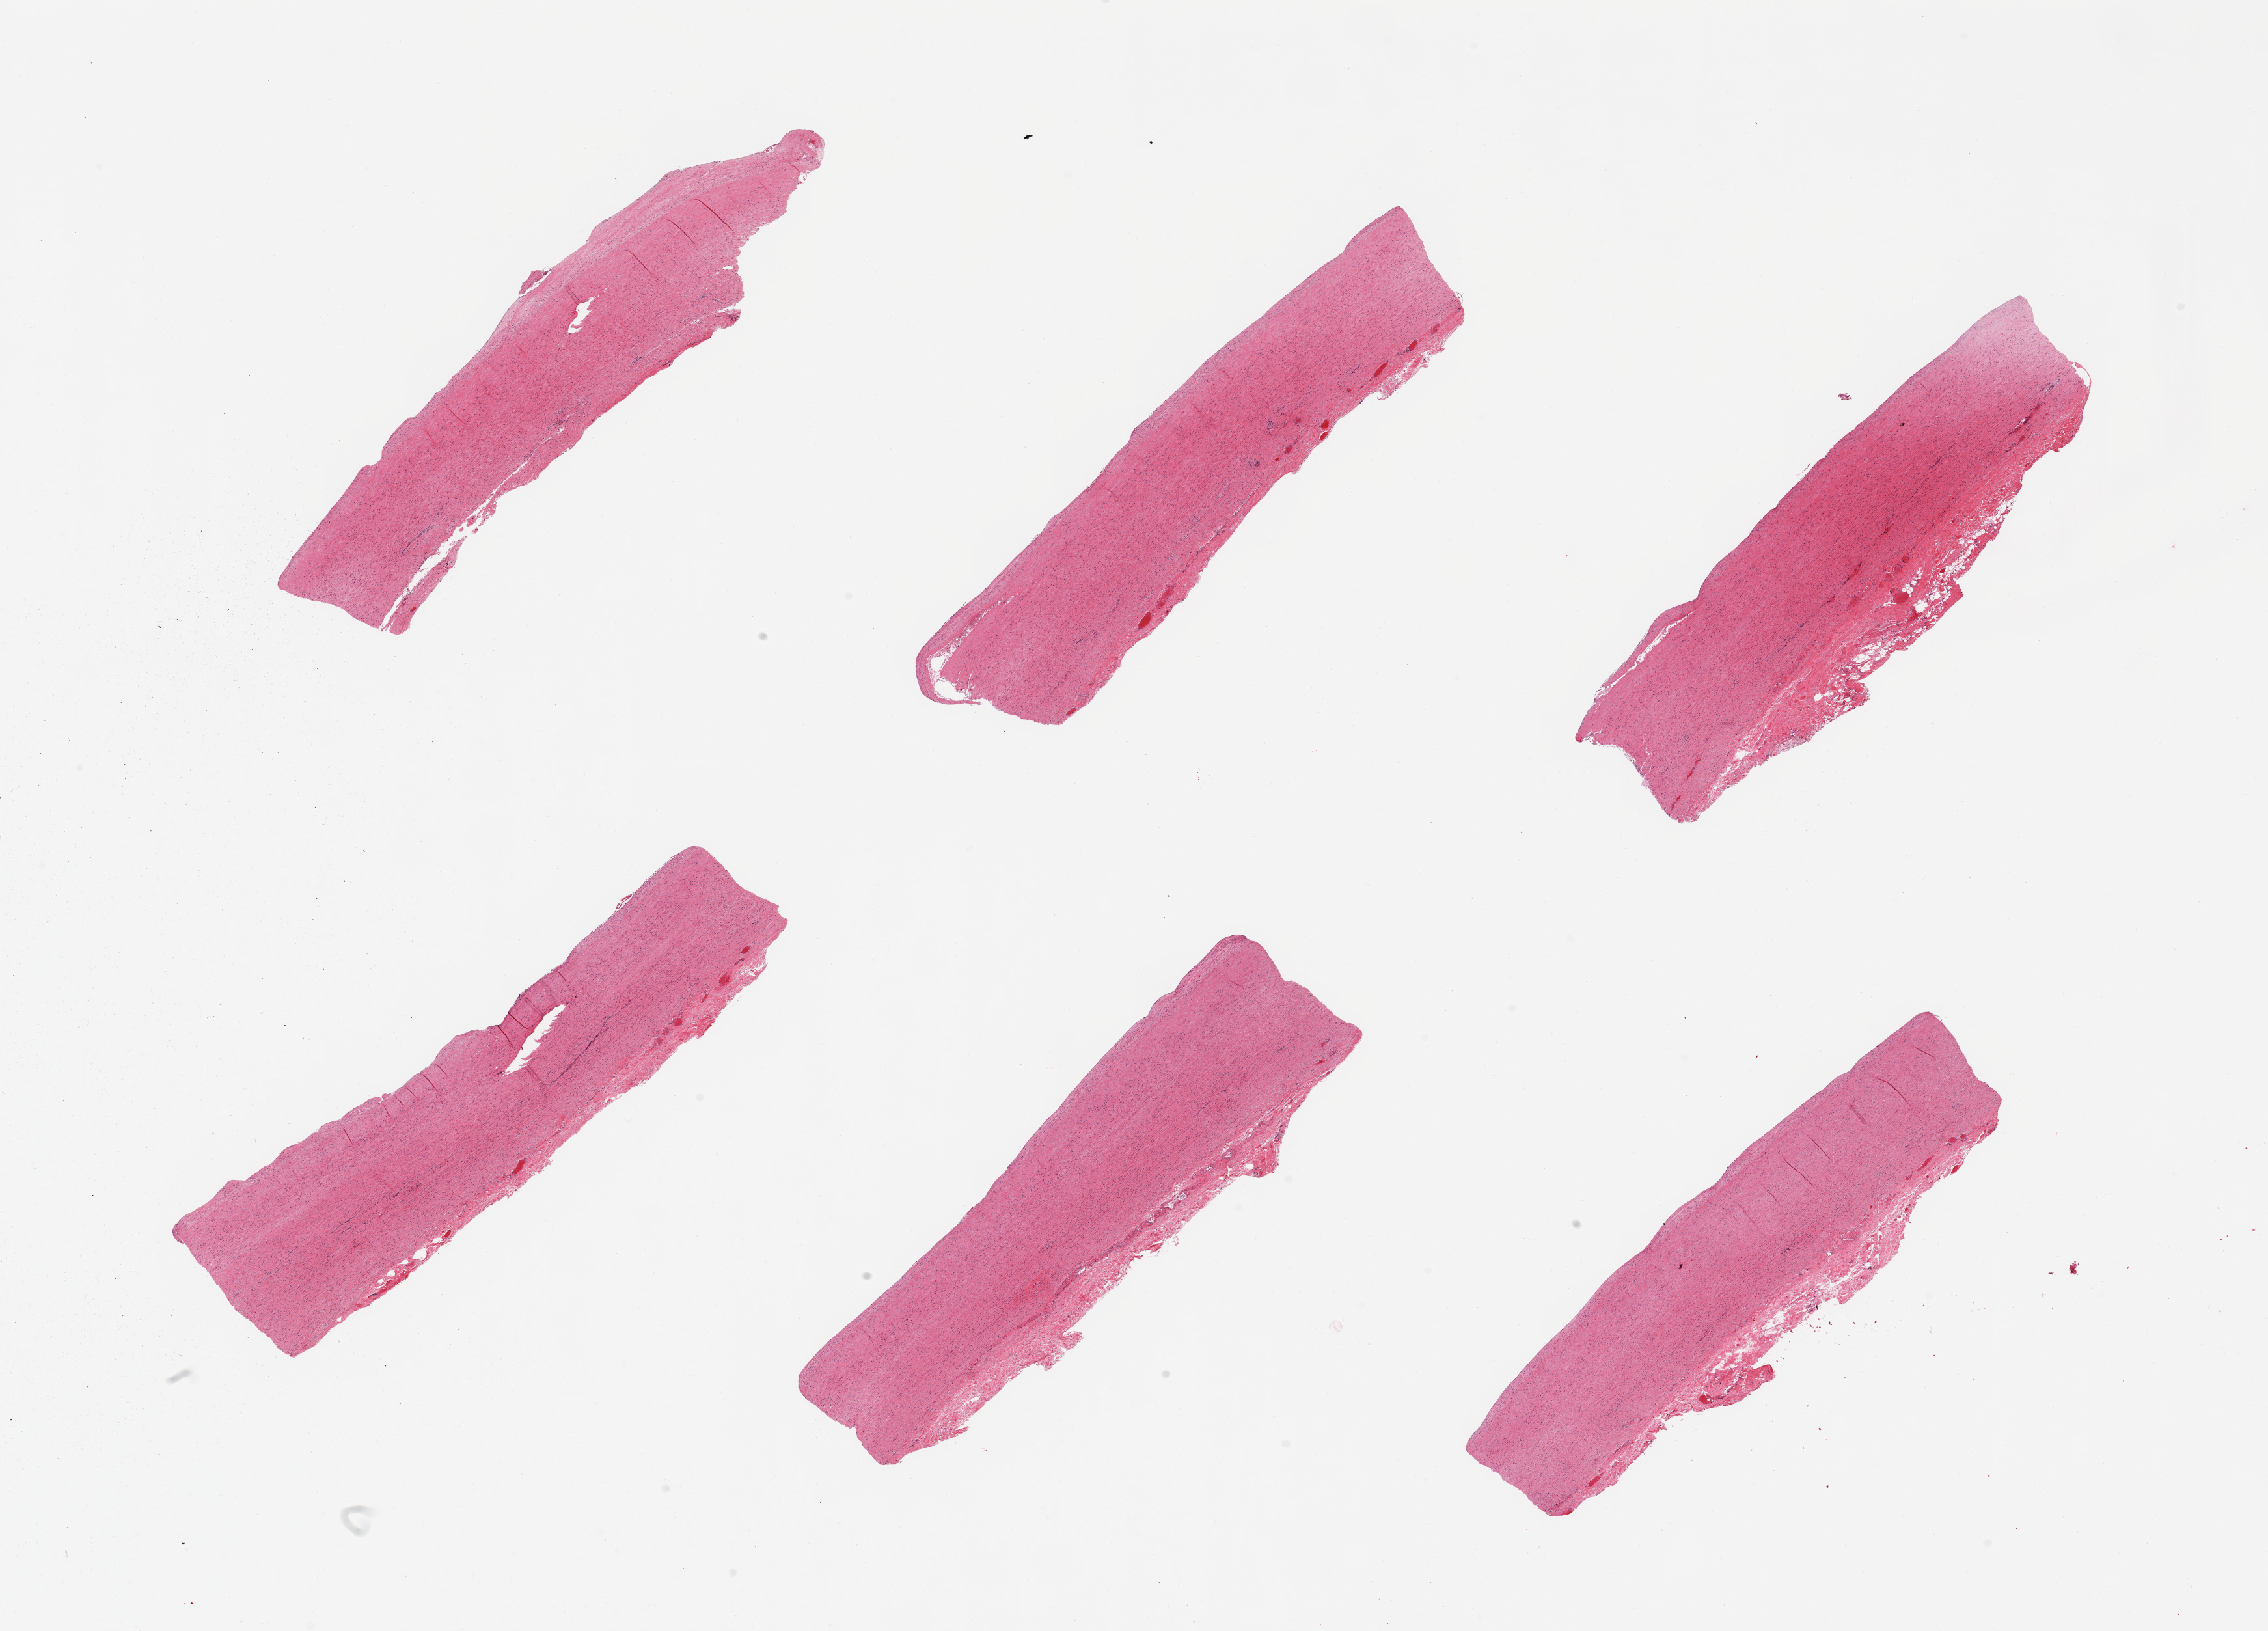
Haematoxylin and eosin whole-slide image — low-resolution overview of the scanned area, about 27.6 x 19.8 mm, PAXgene-fixed, paraffin-embedded tissue, sampled site (target tissue): aorta, donor tissue sample.
Reviewer comment on this tissue sample: 6 pieces; some atherosclerosis.